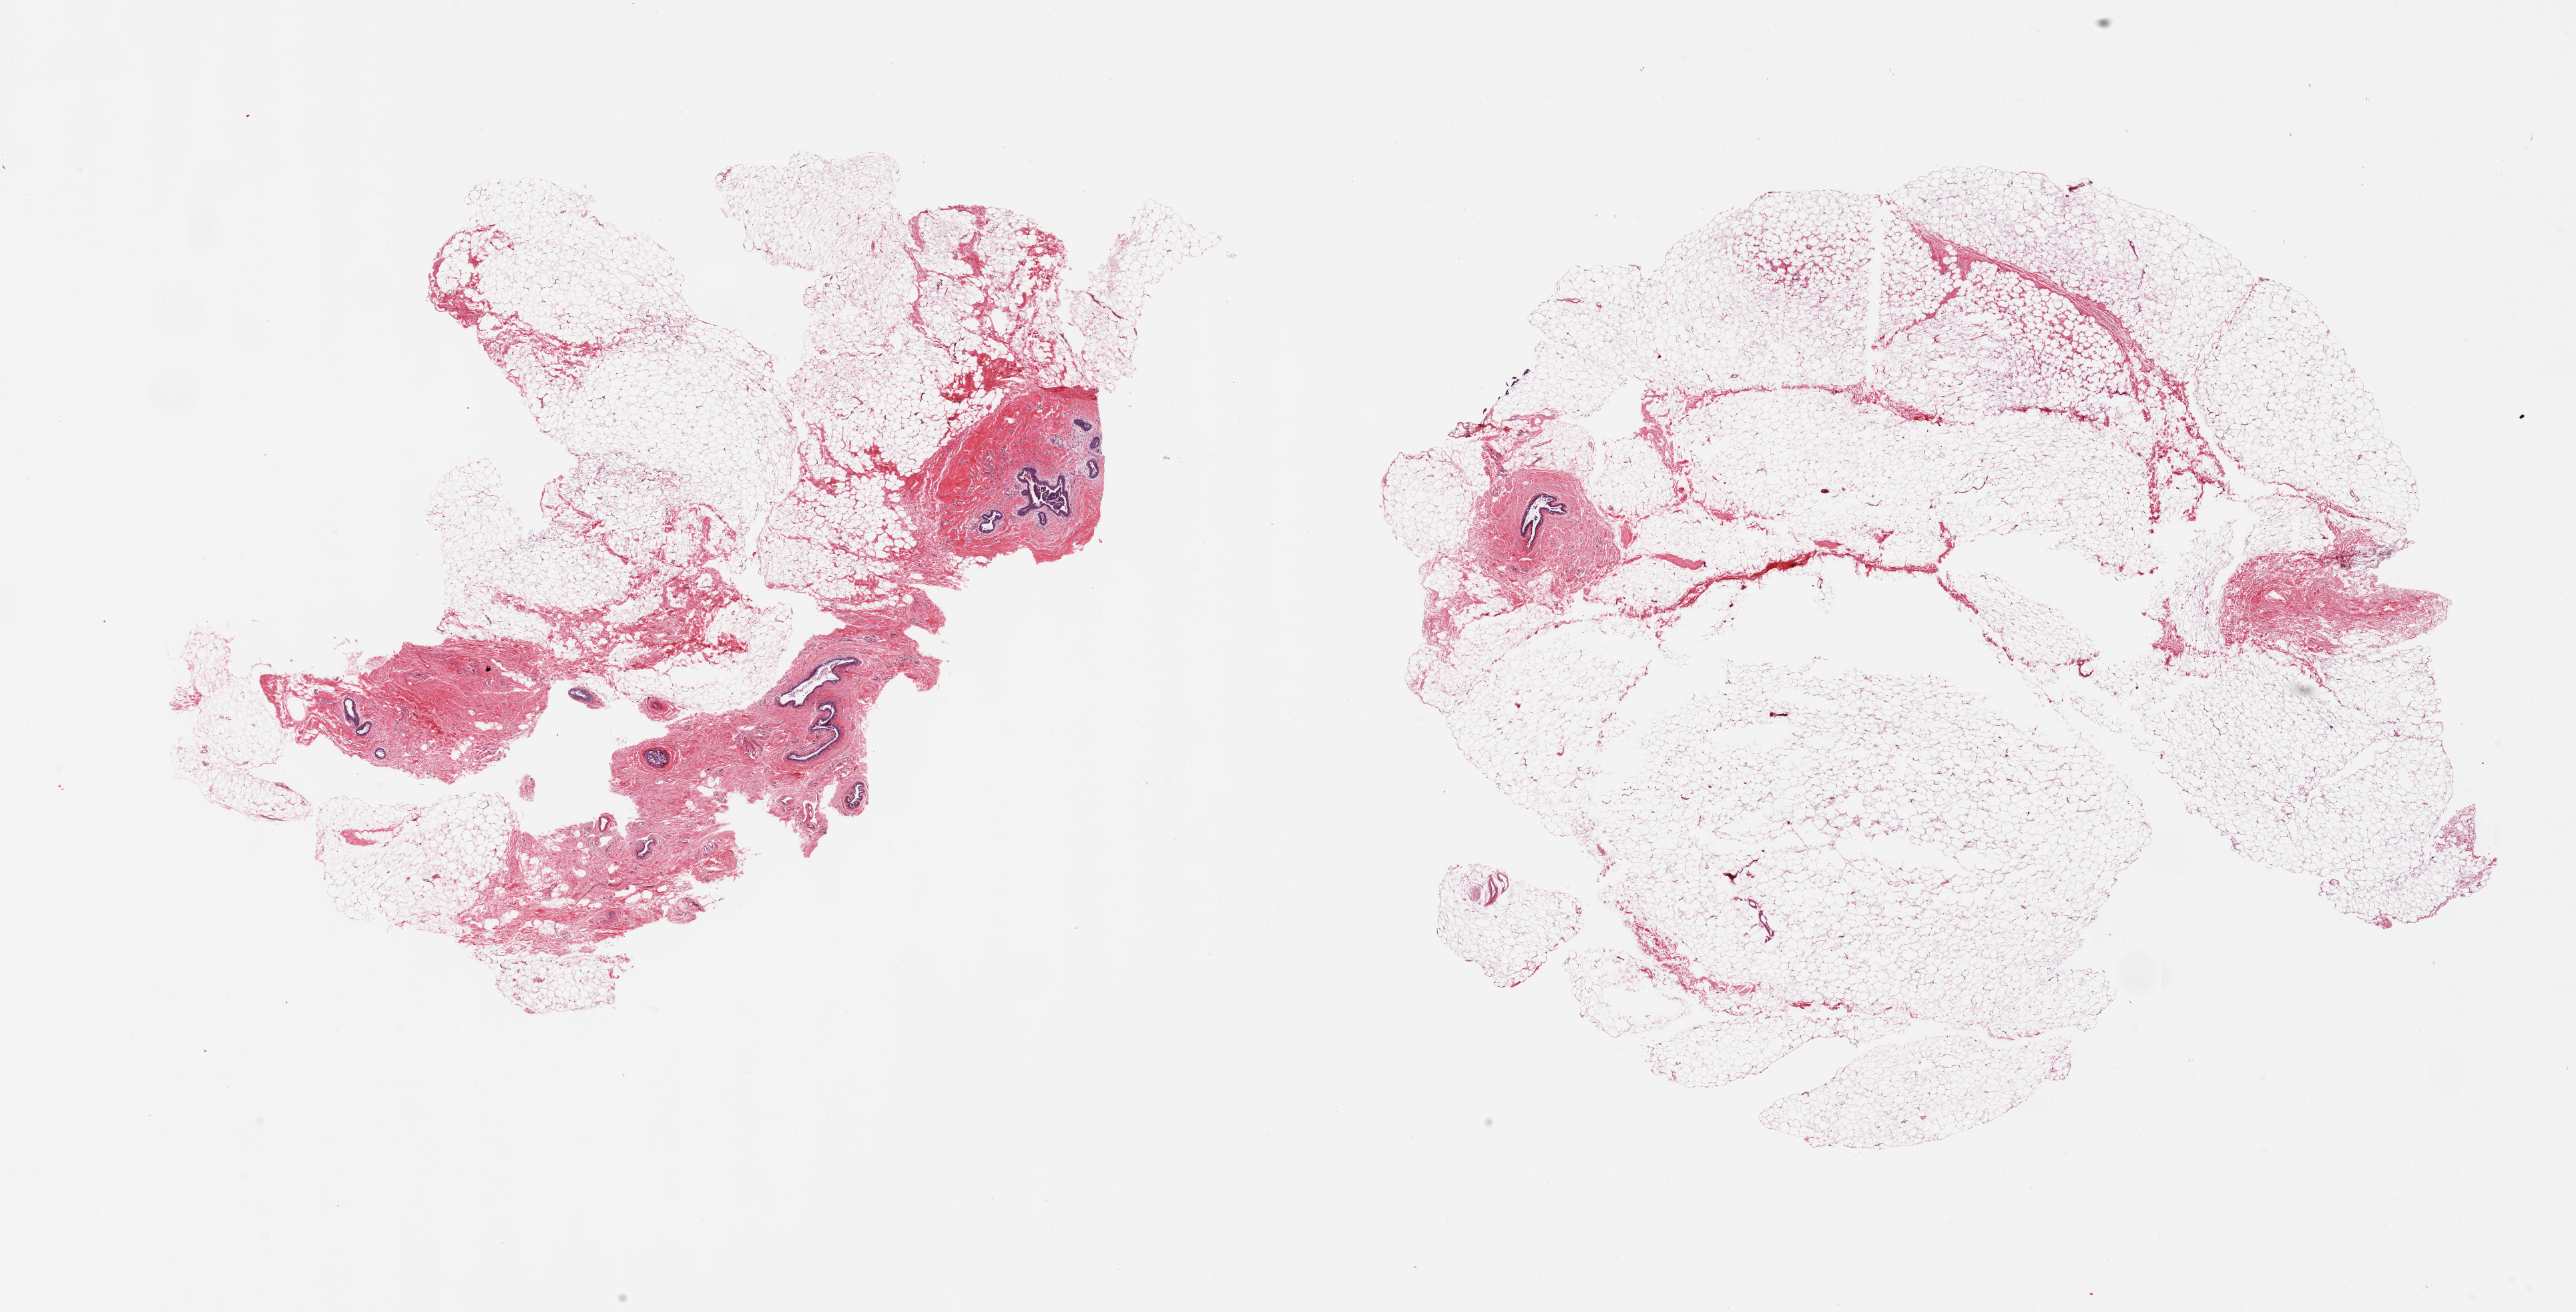
Hematoxylin and eosin (H&E) whole-slide image — whole scanned area (about 30.5 x 15.5 mm) shown as a low-resolution overview, PAXgene-fixed paraffin-embedded (PFPE) section, target tissue: breast, donor tissue sample.
Review note (as recorded): 2 pieces; one represents 60% fat and 40% dense fibrous stroma with scattered ductal structures with focal hyperplasia; other predominantly adipose tissue and ~10% fibrous component with single ductal structure.